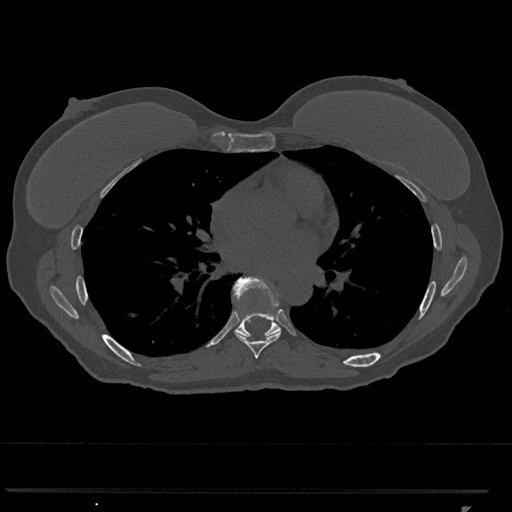
CT including the spine, one axial slice. Position 694 of 793 along the scan axis. Bone window (W 1800 / L 400 HU). 0.5 mm slice thickness. 512 × 512 image matrix, field of view 380 × 380 mm. Patient: female, 62 years. From the clinical record (not read from this slice): primary cancer: renal.
Structures marked on this image (semi-automatic segmentation, software-assisted and operator-edited):
- T7 vertebra: box from (x=234, y=286) to (x=281, y=359) px
- T8 vertebra: (x=233, y=276)–(x=281, y=337)